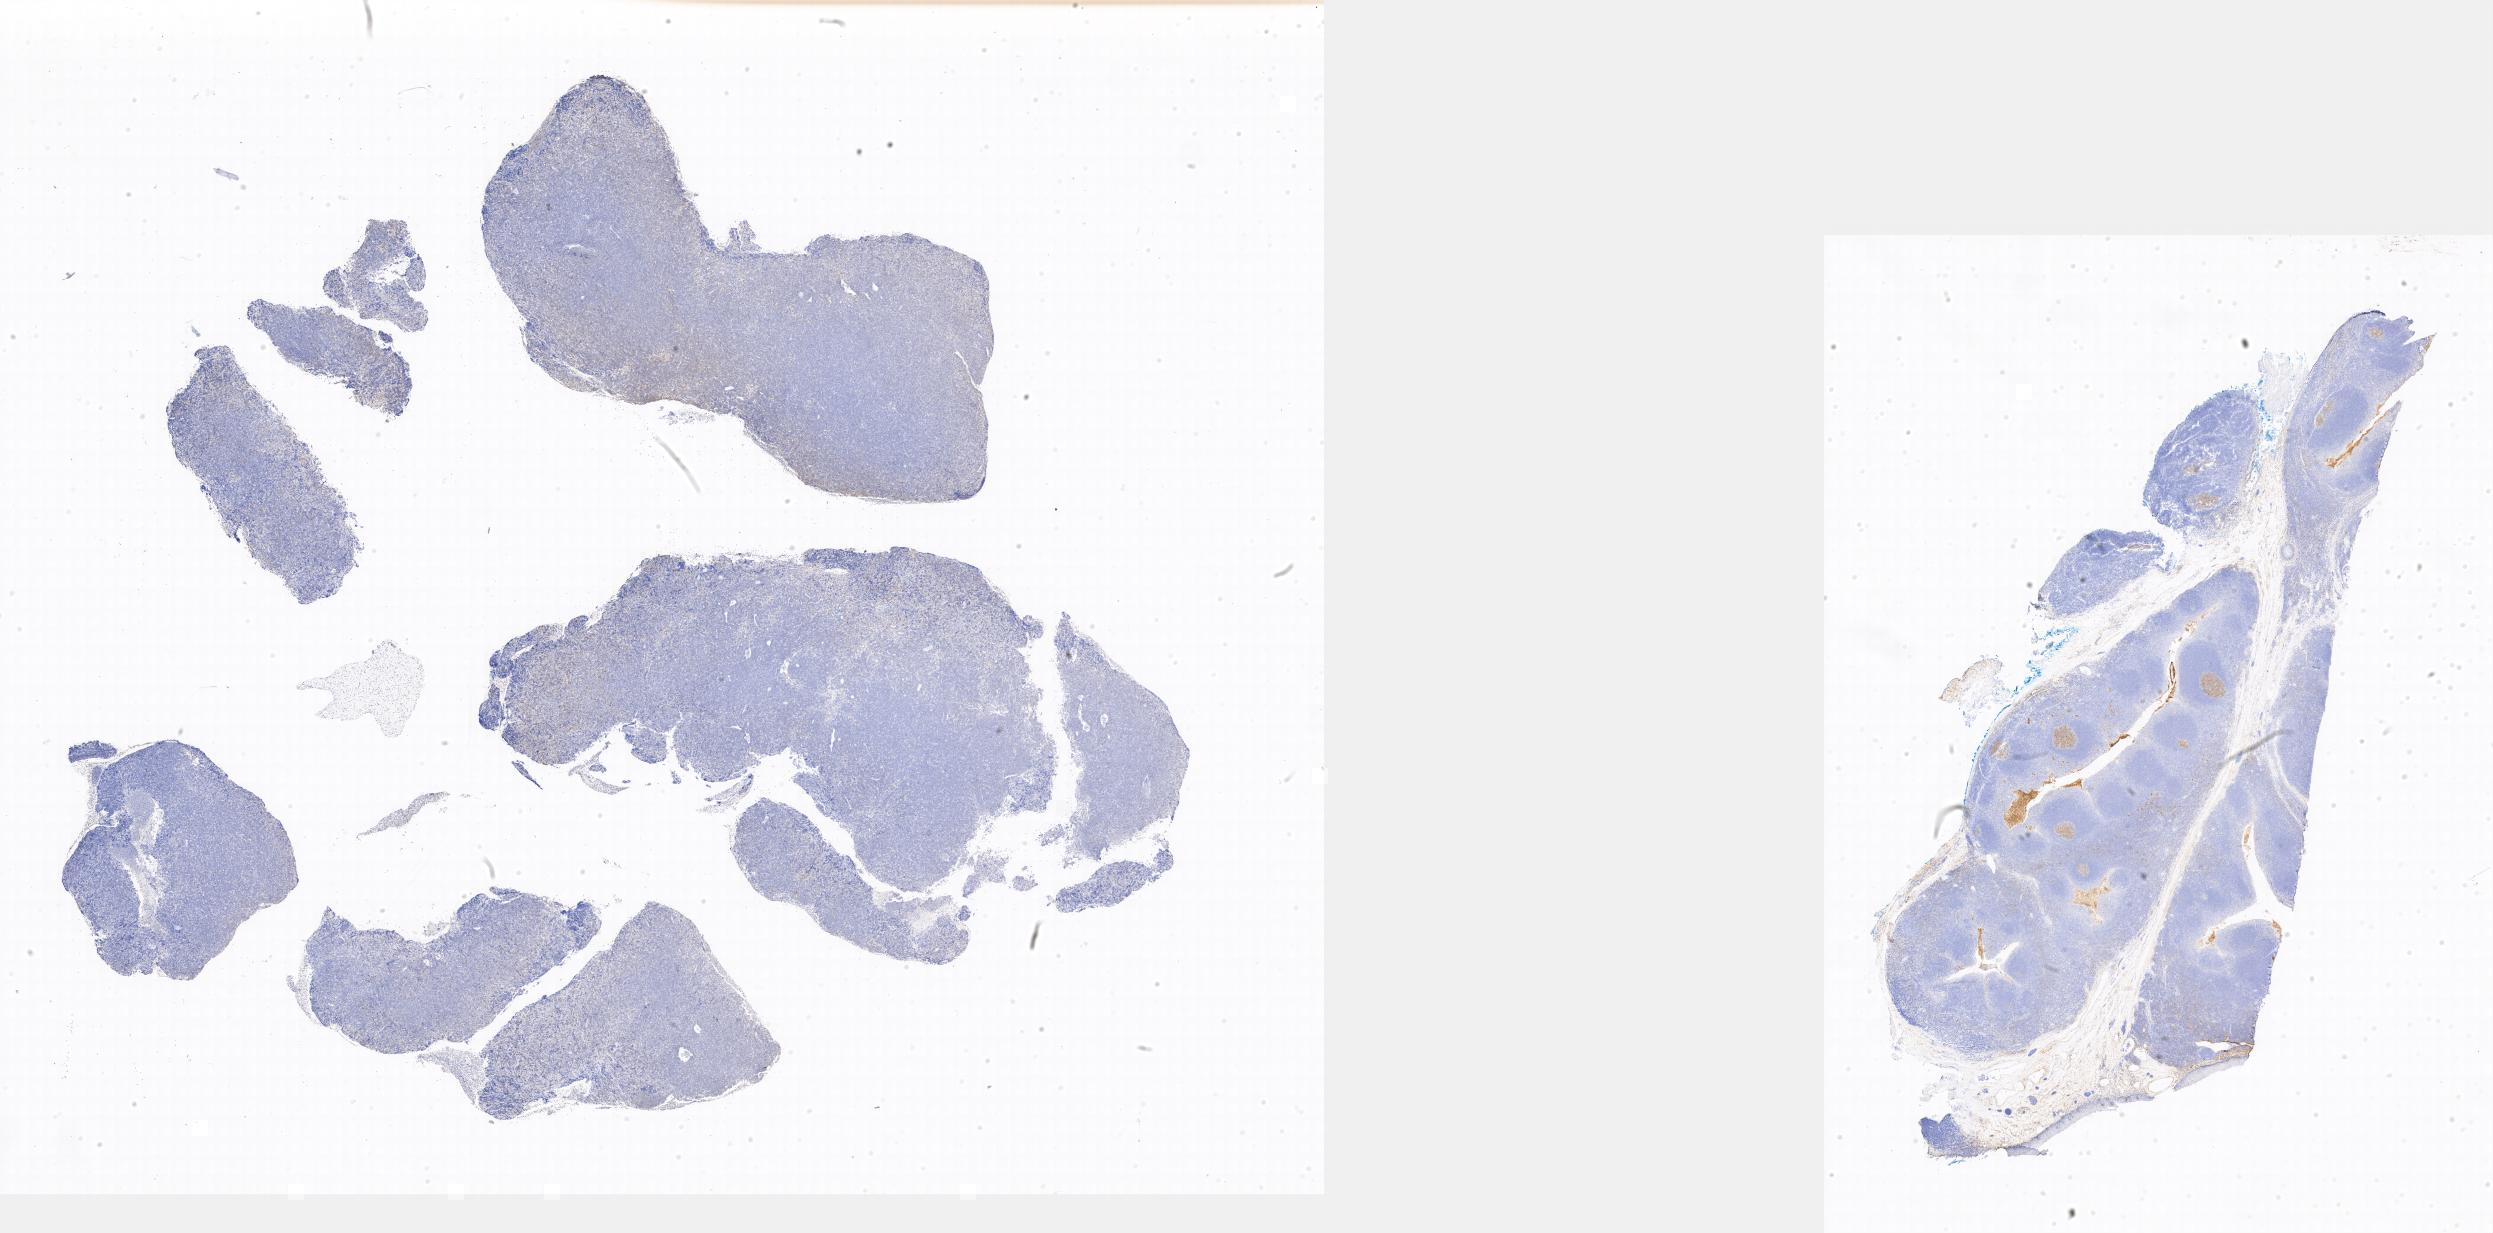
Immunohistochemistry (IHC) whole-slide image stained for CD10 — a low-resolution overview of the entire scanned area; specimen: tumor tissue; site: soft tissue. Female patient; age at initial diagnosis 9 years.
Diagnosis: Burkitt lymphoma, NOS.